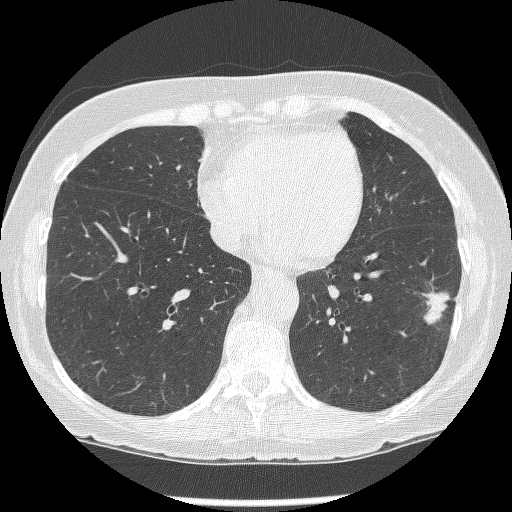
Axial slice from a low-dose chest CT screening exam; baseline screening round; lung window (W 1500 / L -600 HU); 1.25 mm slice thickness; lung (sharp) reconstruction kernel (BONE); slice 88 of 247 in the series. Female, age 62 years at enrolment. Former smoker at enrolment.
Expert-annotated lung lesion, bounding box (x1, y1, x2, y2) in pixels: (420, 282, 462, 328). The screening reader recorded 2 non-calcified nodules or masses ≥4 mm on this exam; which of them this box marks is not recorded.